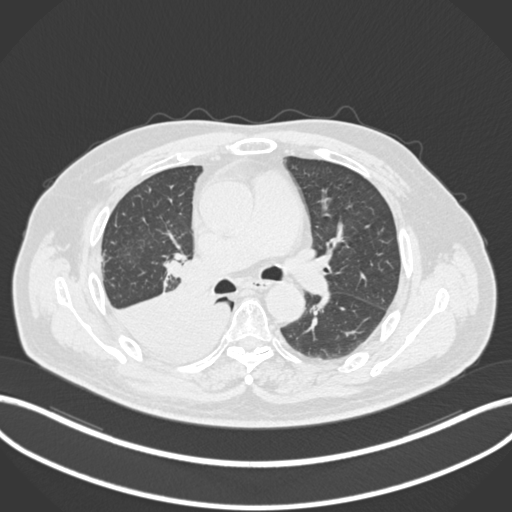
Chest CT, one axial slice; position 115 of 218 along the scan axis; reconstruction kernel B30f; 120 kVp; lung window (W 1500 / L -600 HU); 1 mm slice thickness; 512 × 512 image matrix, field of view 400 × 400 mm. Patient: male, 68 years. Case-level facts recorded for this patient, not image findings: clinical TNM (as recorded): T2a N0 M0.
Outlined on this slice (rectangle marked by the reading radiologist):
- lung tumour (recorded histology: adenocarcinoma): bounding box (x1, y1, x2, y2) in pixels: (108, 286, 232, 369)